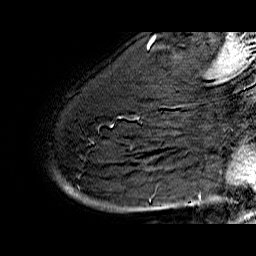
Breast MRI (dynamic contrast-enhanced), one sagittal slice; slice 48 of 60 in the series (ordered by position); dynamic contrast-enhanced series, time point 2 of 6 at this slice position (early post-contrast); 1.5 T; TE 6.4 ms, TR 32.9 ms; 4 mm slice thickness; 256 × 256 image matrix. Female patient. Case-level facts recorded for this patient, not image findings: setting: breast cancer imaged before/during neoadjuvant chemotherapy; receptor status: HR-positive, HER2-negative.
Structures marked on this image (semi-automatic segmentation, software-assisted and operator-edited):
- analysis volume of interest (the breast-tissue region the enhancement analysis was run in; not a lesion): bounding box (x1, y1, x2, y2) in pixels: (57, 74, 176, 210)
- tumour enhancement mask (voxels above the 100 % enhancement threshold inside the analysis volume of interest): (65, 187, 72, 195)